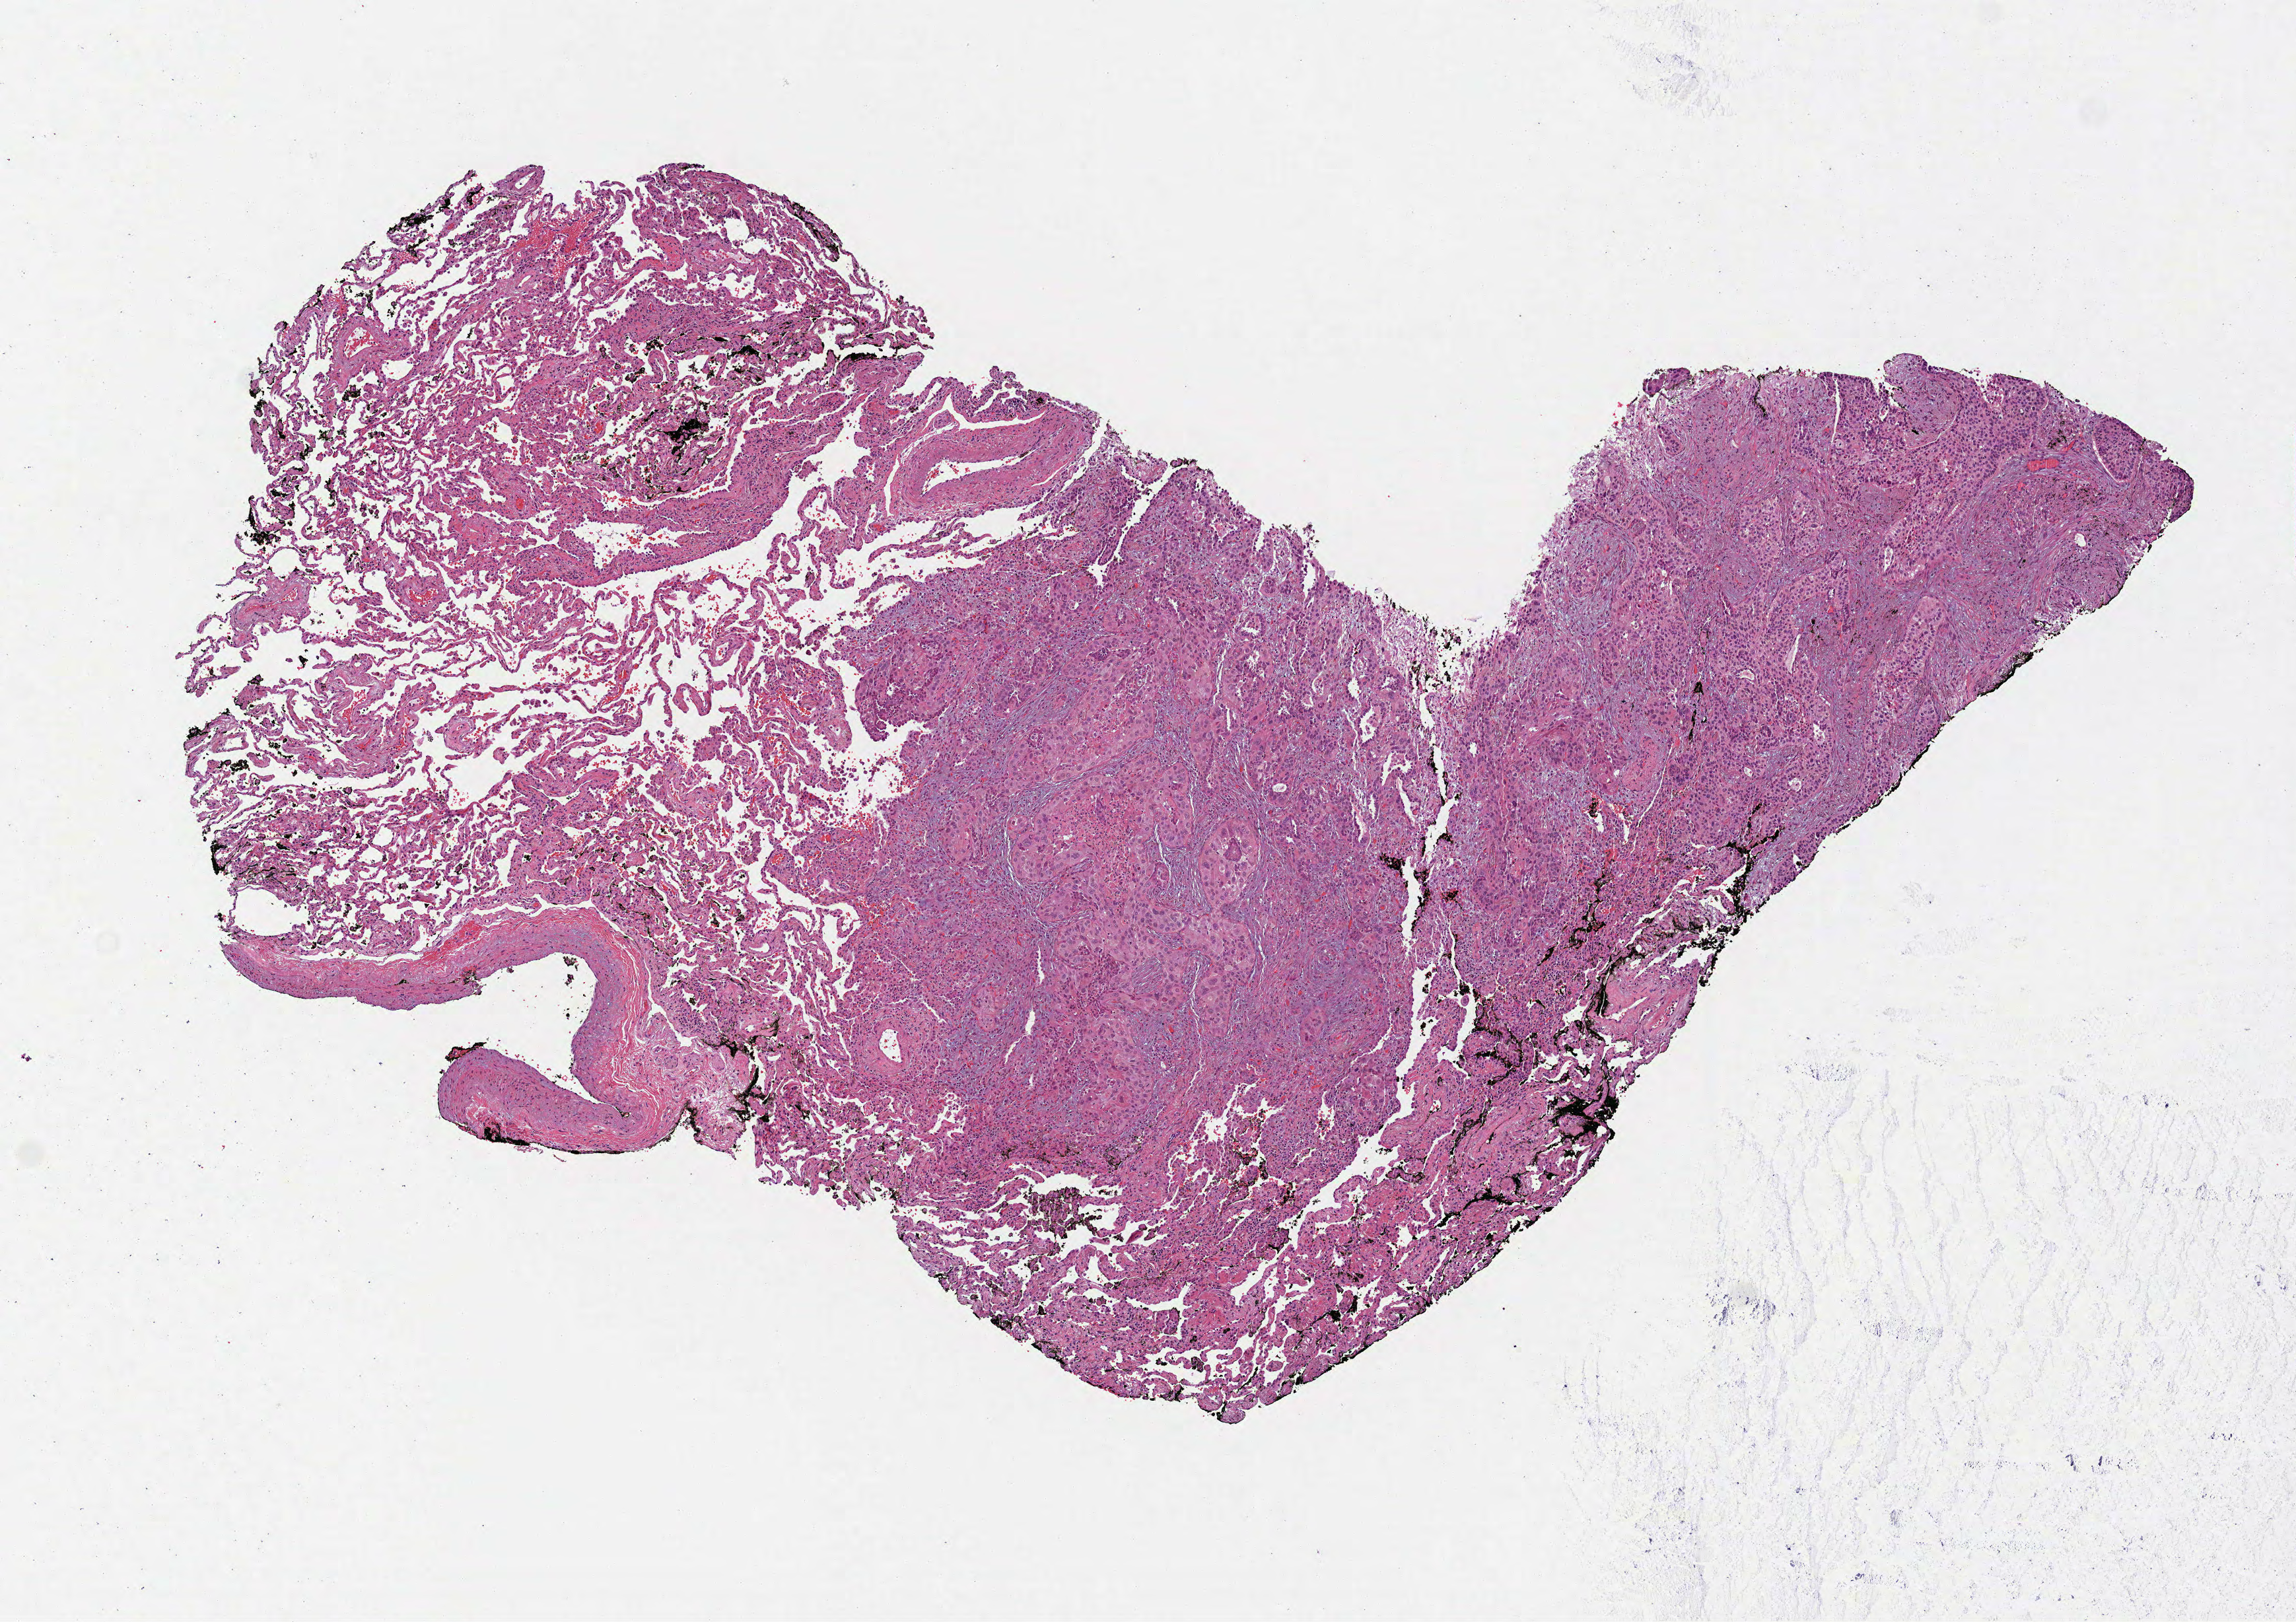
Whole-slide histology image, Hematoxylin and eosin (H&E) stained — low-resolution overview of the scanned area, about 7.0 x 5.0 mm (acquisition: 40x scan). FFPE section. Sample: primary tumour, lung. Female, age 75 years at initial diagnosis.
AJCC pathologic stage: IA. Histologic diagnosis: Squamous cell carcinoma, large cell, nonkeratinizing, NOS (lower lobe, lung).